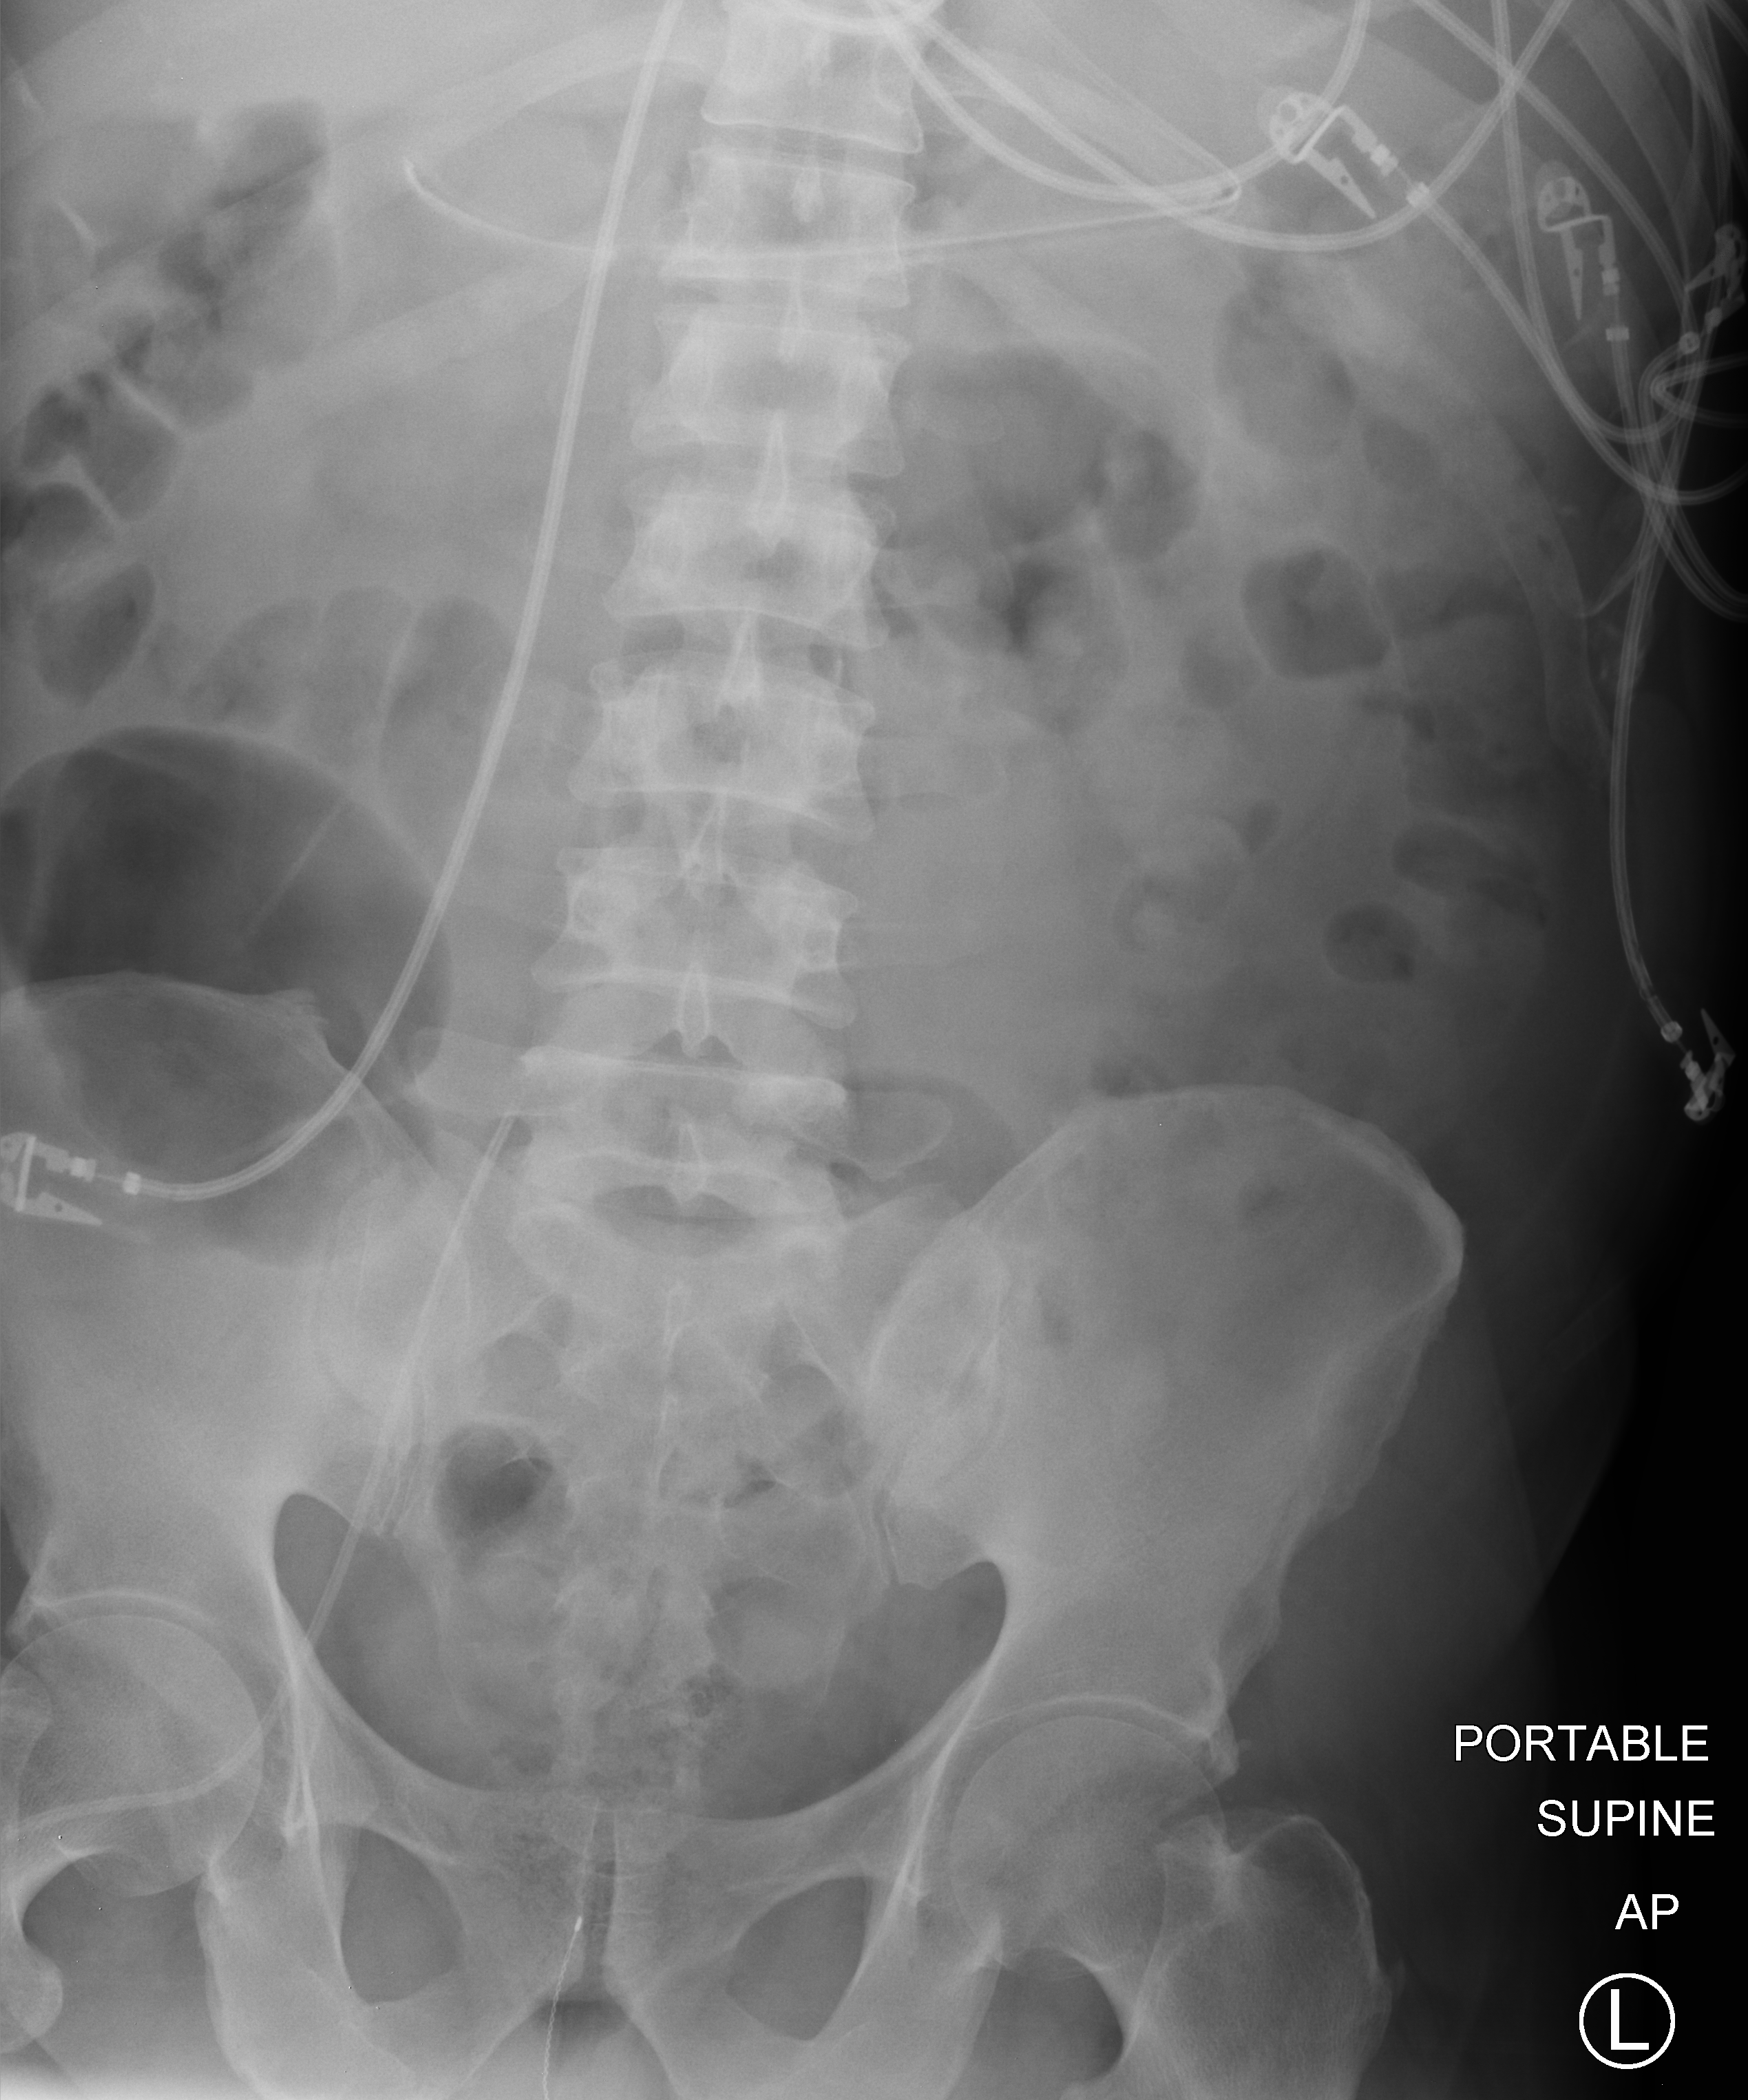
Abdomen X-ray (portable), anteroposterior (AP) projection. Male patient hospitalised with COVID-19, age 18–59 years.
From the hospital-stay record, not from the radiograph (when in the stay this image was taken is not recorded): COPD (admission record): no.